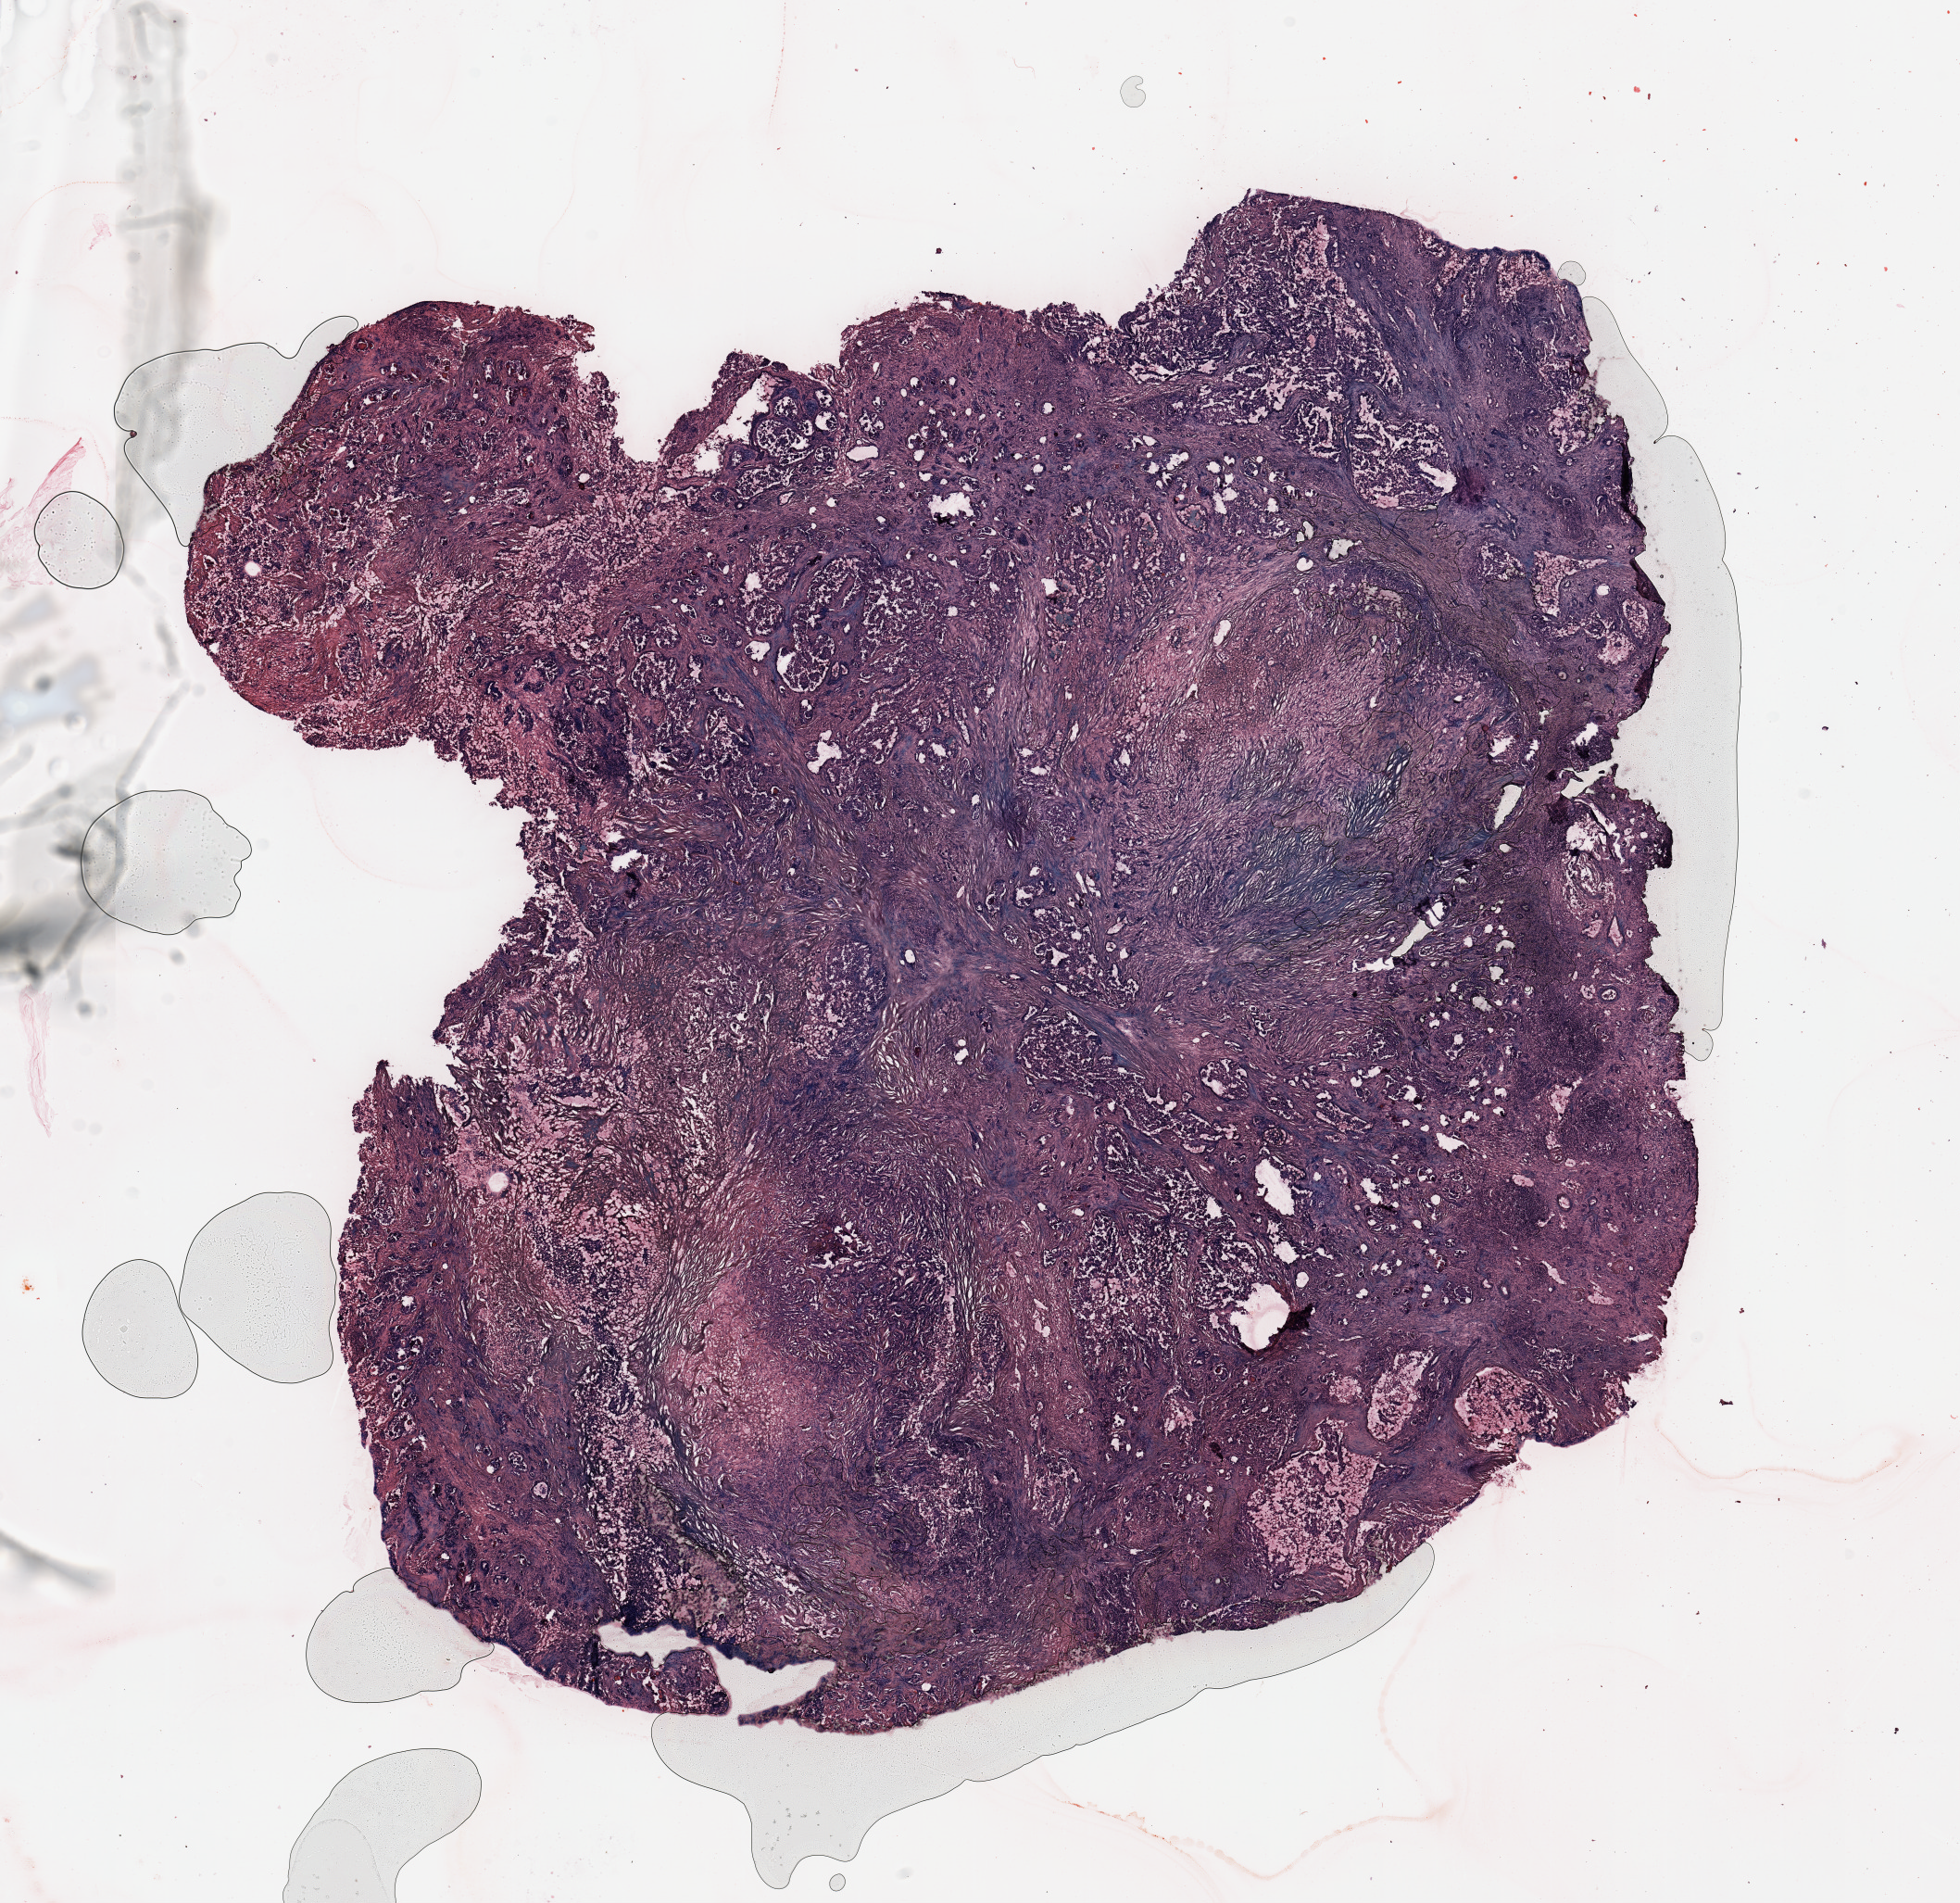
Whole-slide histology image, Hematoxylin and eosin (H&E) stained — low-resolution overview of the scanned area, about 16.7 x 16.2 mm (slide scanned at 20x). Tumour tissue sample, kidney. Patient: male, age 72 years. Histologic grade: G3 (poorly differentiated).
* AJCC pathologic stage: III
* primary tumour site (as recorded): upper pole
* histologic diagnosis: Renal cell carcinoma, NOS